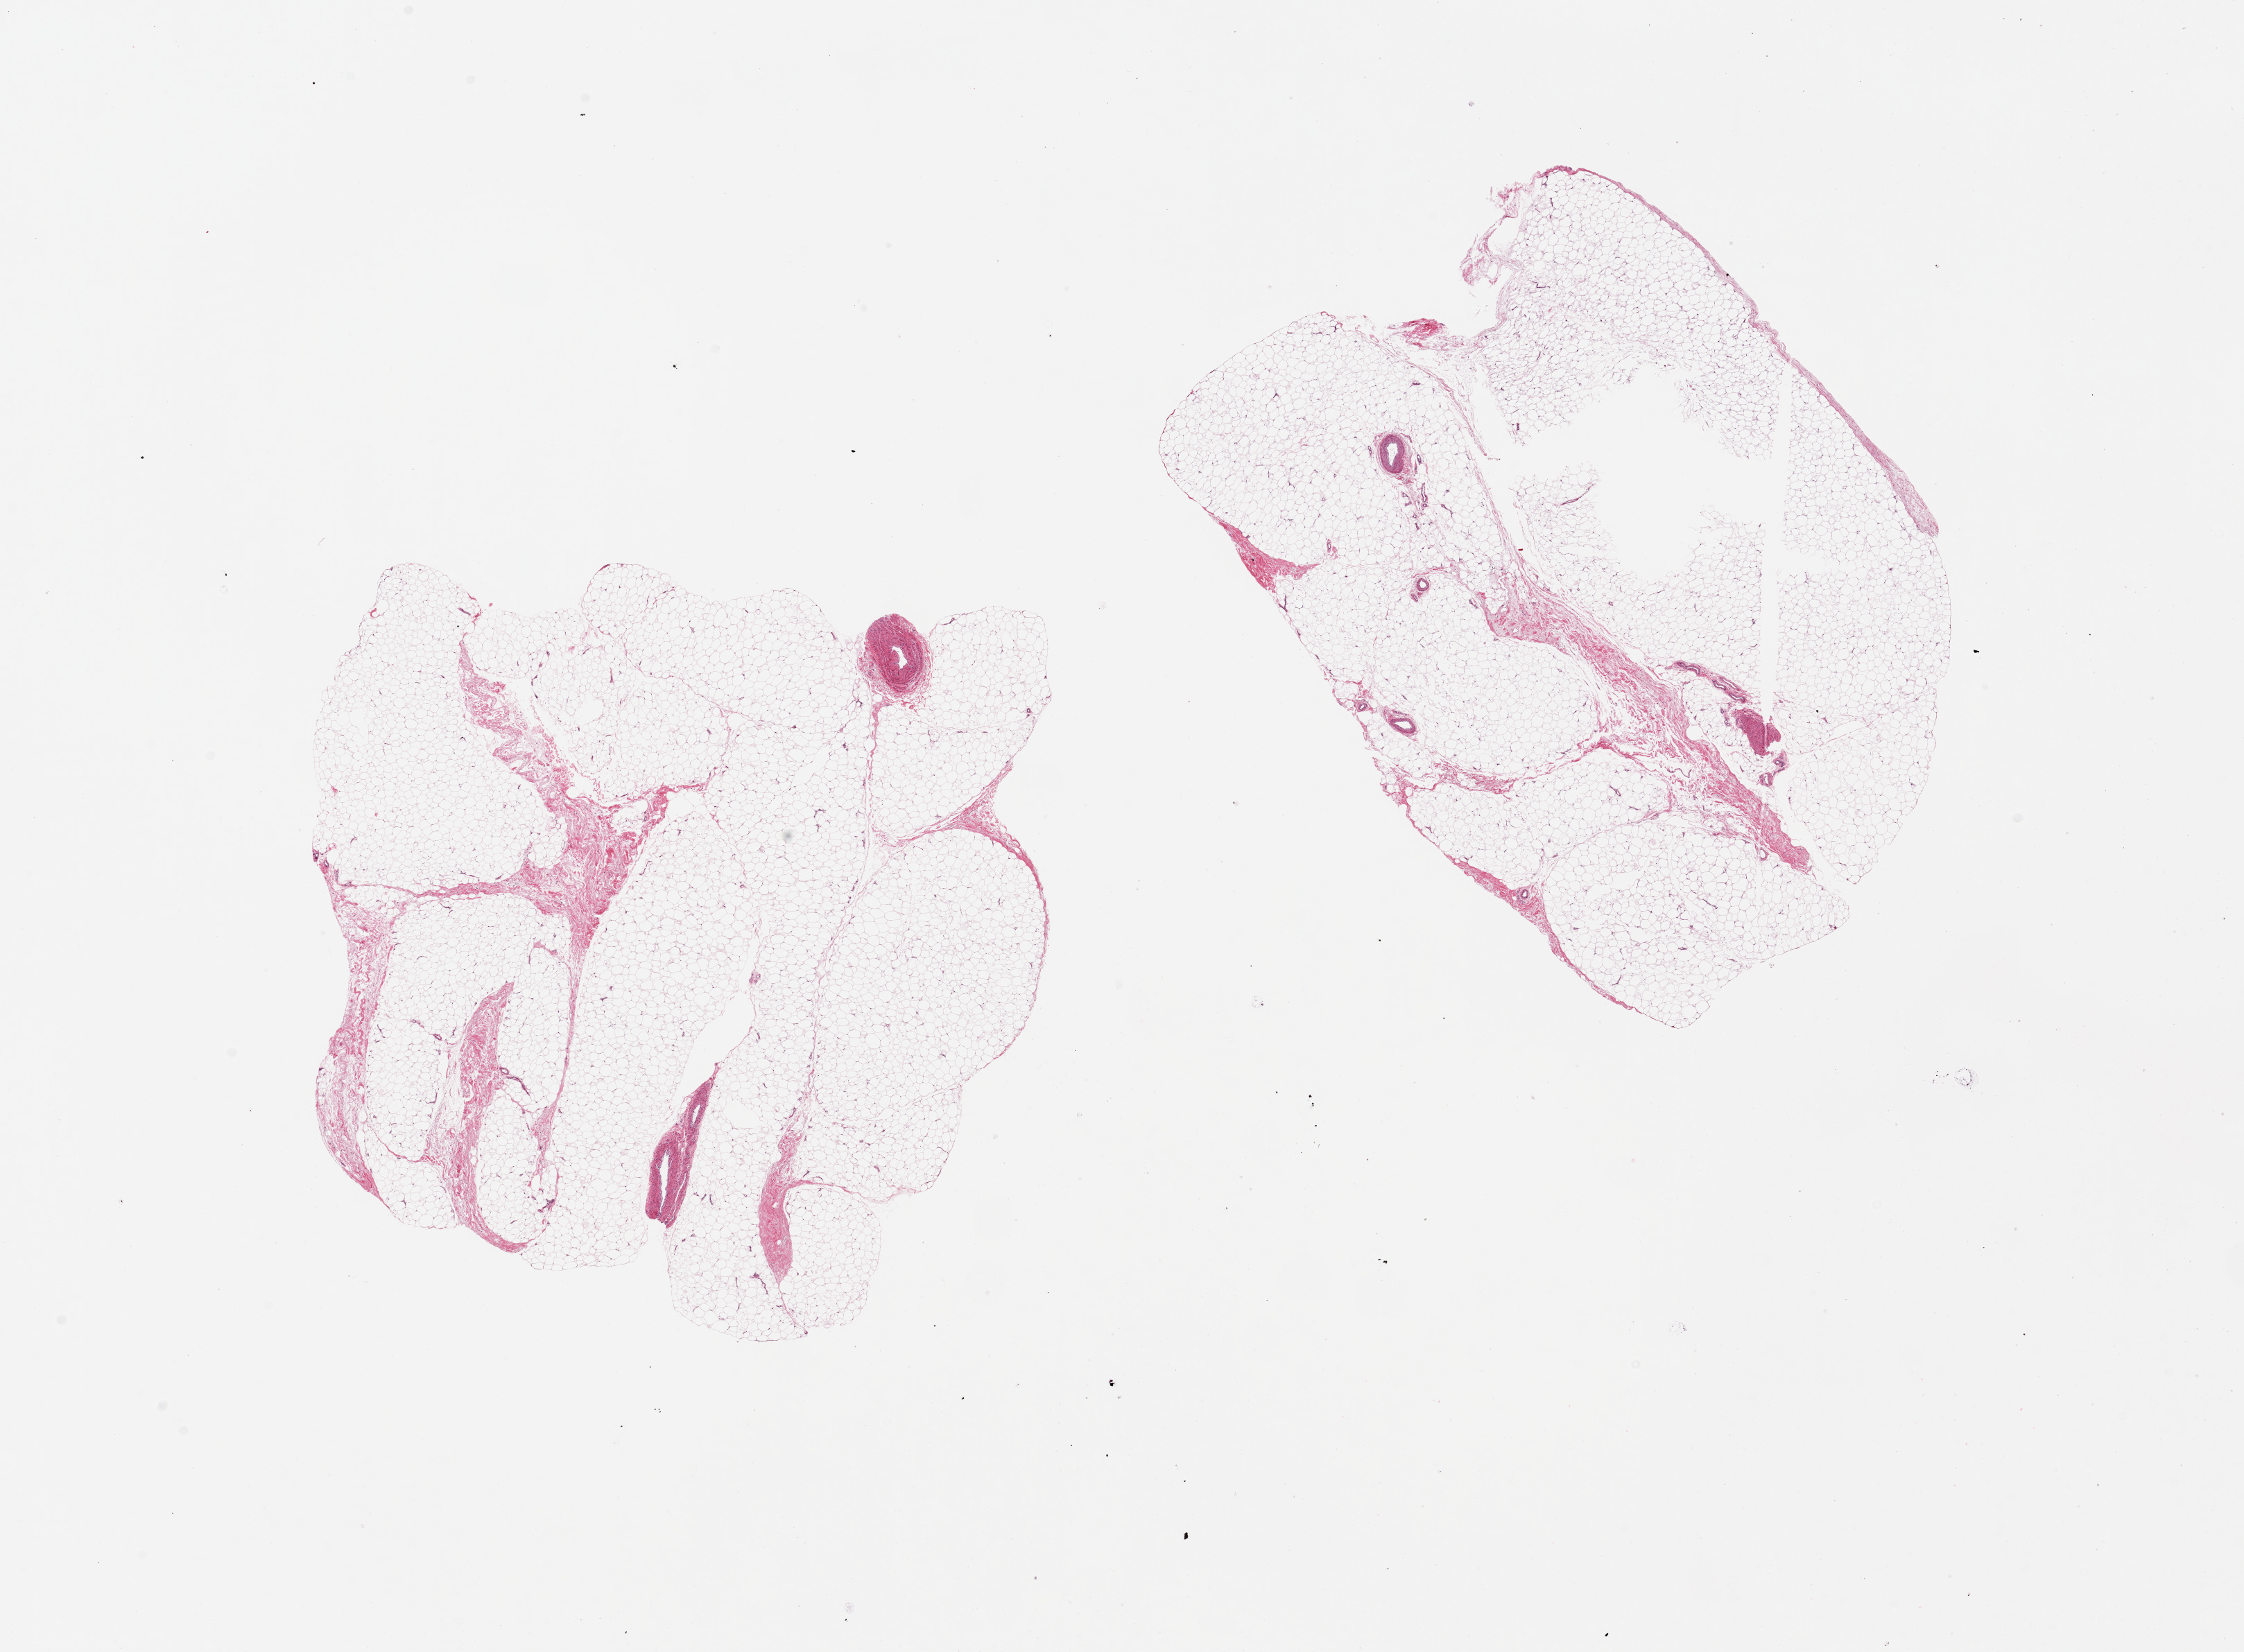
Whole-slide image, H&E stain, low-resolution overview of the scanned area, about 25.6 x 18.8 mm (acquisition: 20x scan), PAXgene-fixed paraffin-embedded (PFPE) section, target tissue: adipose tissue, tissue donor sample. Male donor.
* pathologist's review note for this sample: 2 pieces, 9x9 & 9x7mm; several centrall holes